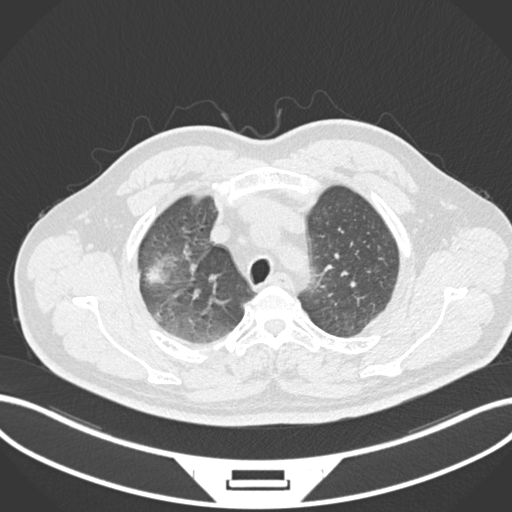
Chest CT, one axial slice. Slice 685 of 852 in the series (ordered by position). Reconstruction kernel B30f. 120 kVp. Lung window (W 1500 / L -600 HU). 1 mm slice thickness. 512 × 512 image matrix, field of view 400 × 400 mm. Male patient, age 55 years. From the clinical record (not read from this slice): clinical TNM (as recorded): T3 N2 M1.
Structures marked on this image (rectangle marked by the reading radiologist):
- lung tumour (recorded histology: adenocarcinoma): box from (x=144, y=261) to (x=172, y=287) px